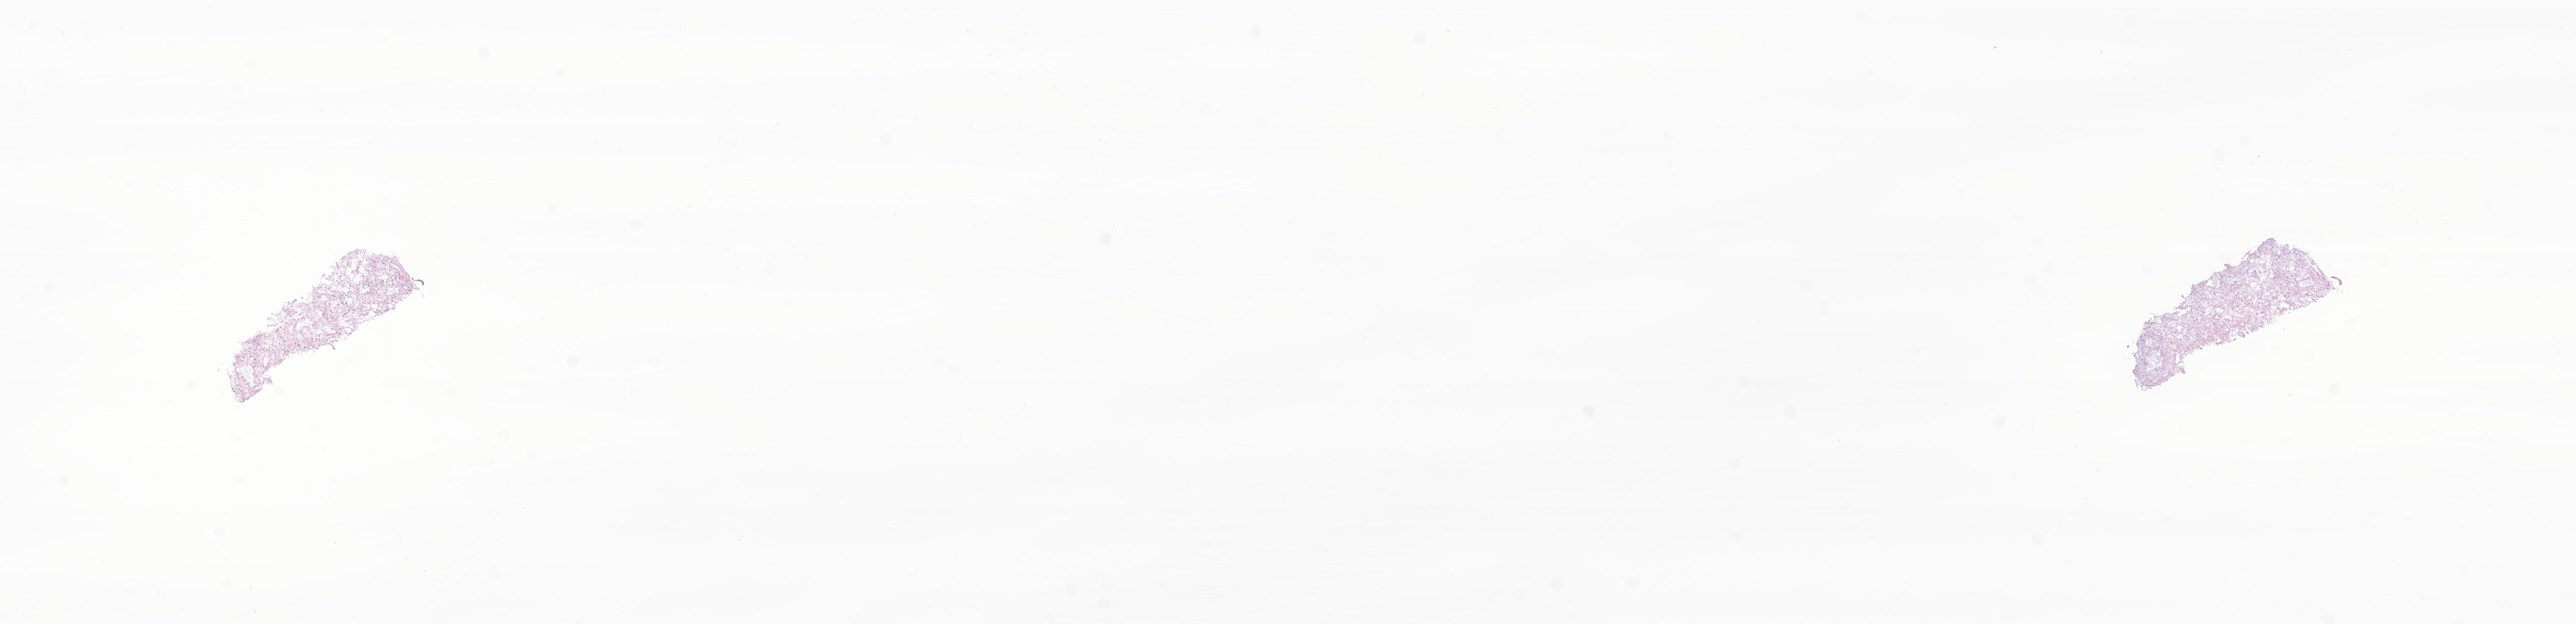
Whole-slide image, H&E stain of tumor tissue from the brain, a low-resolution overview of the entire scanned area, about 21.7 x 5.3 mm. Cryosection (OCT / tissue freezing medium). Male patient, age 189 months (15 years 9 months).
Recorded diagnosis: Pilocytic astrocytoma.